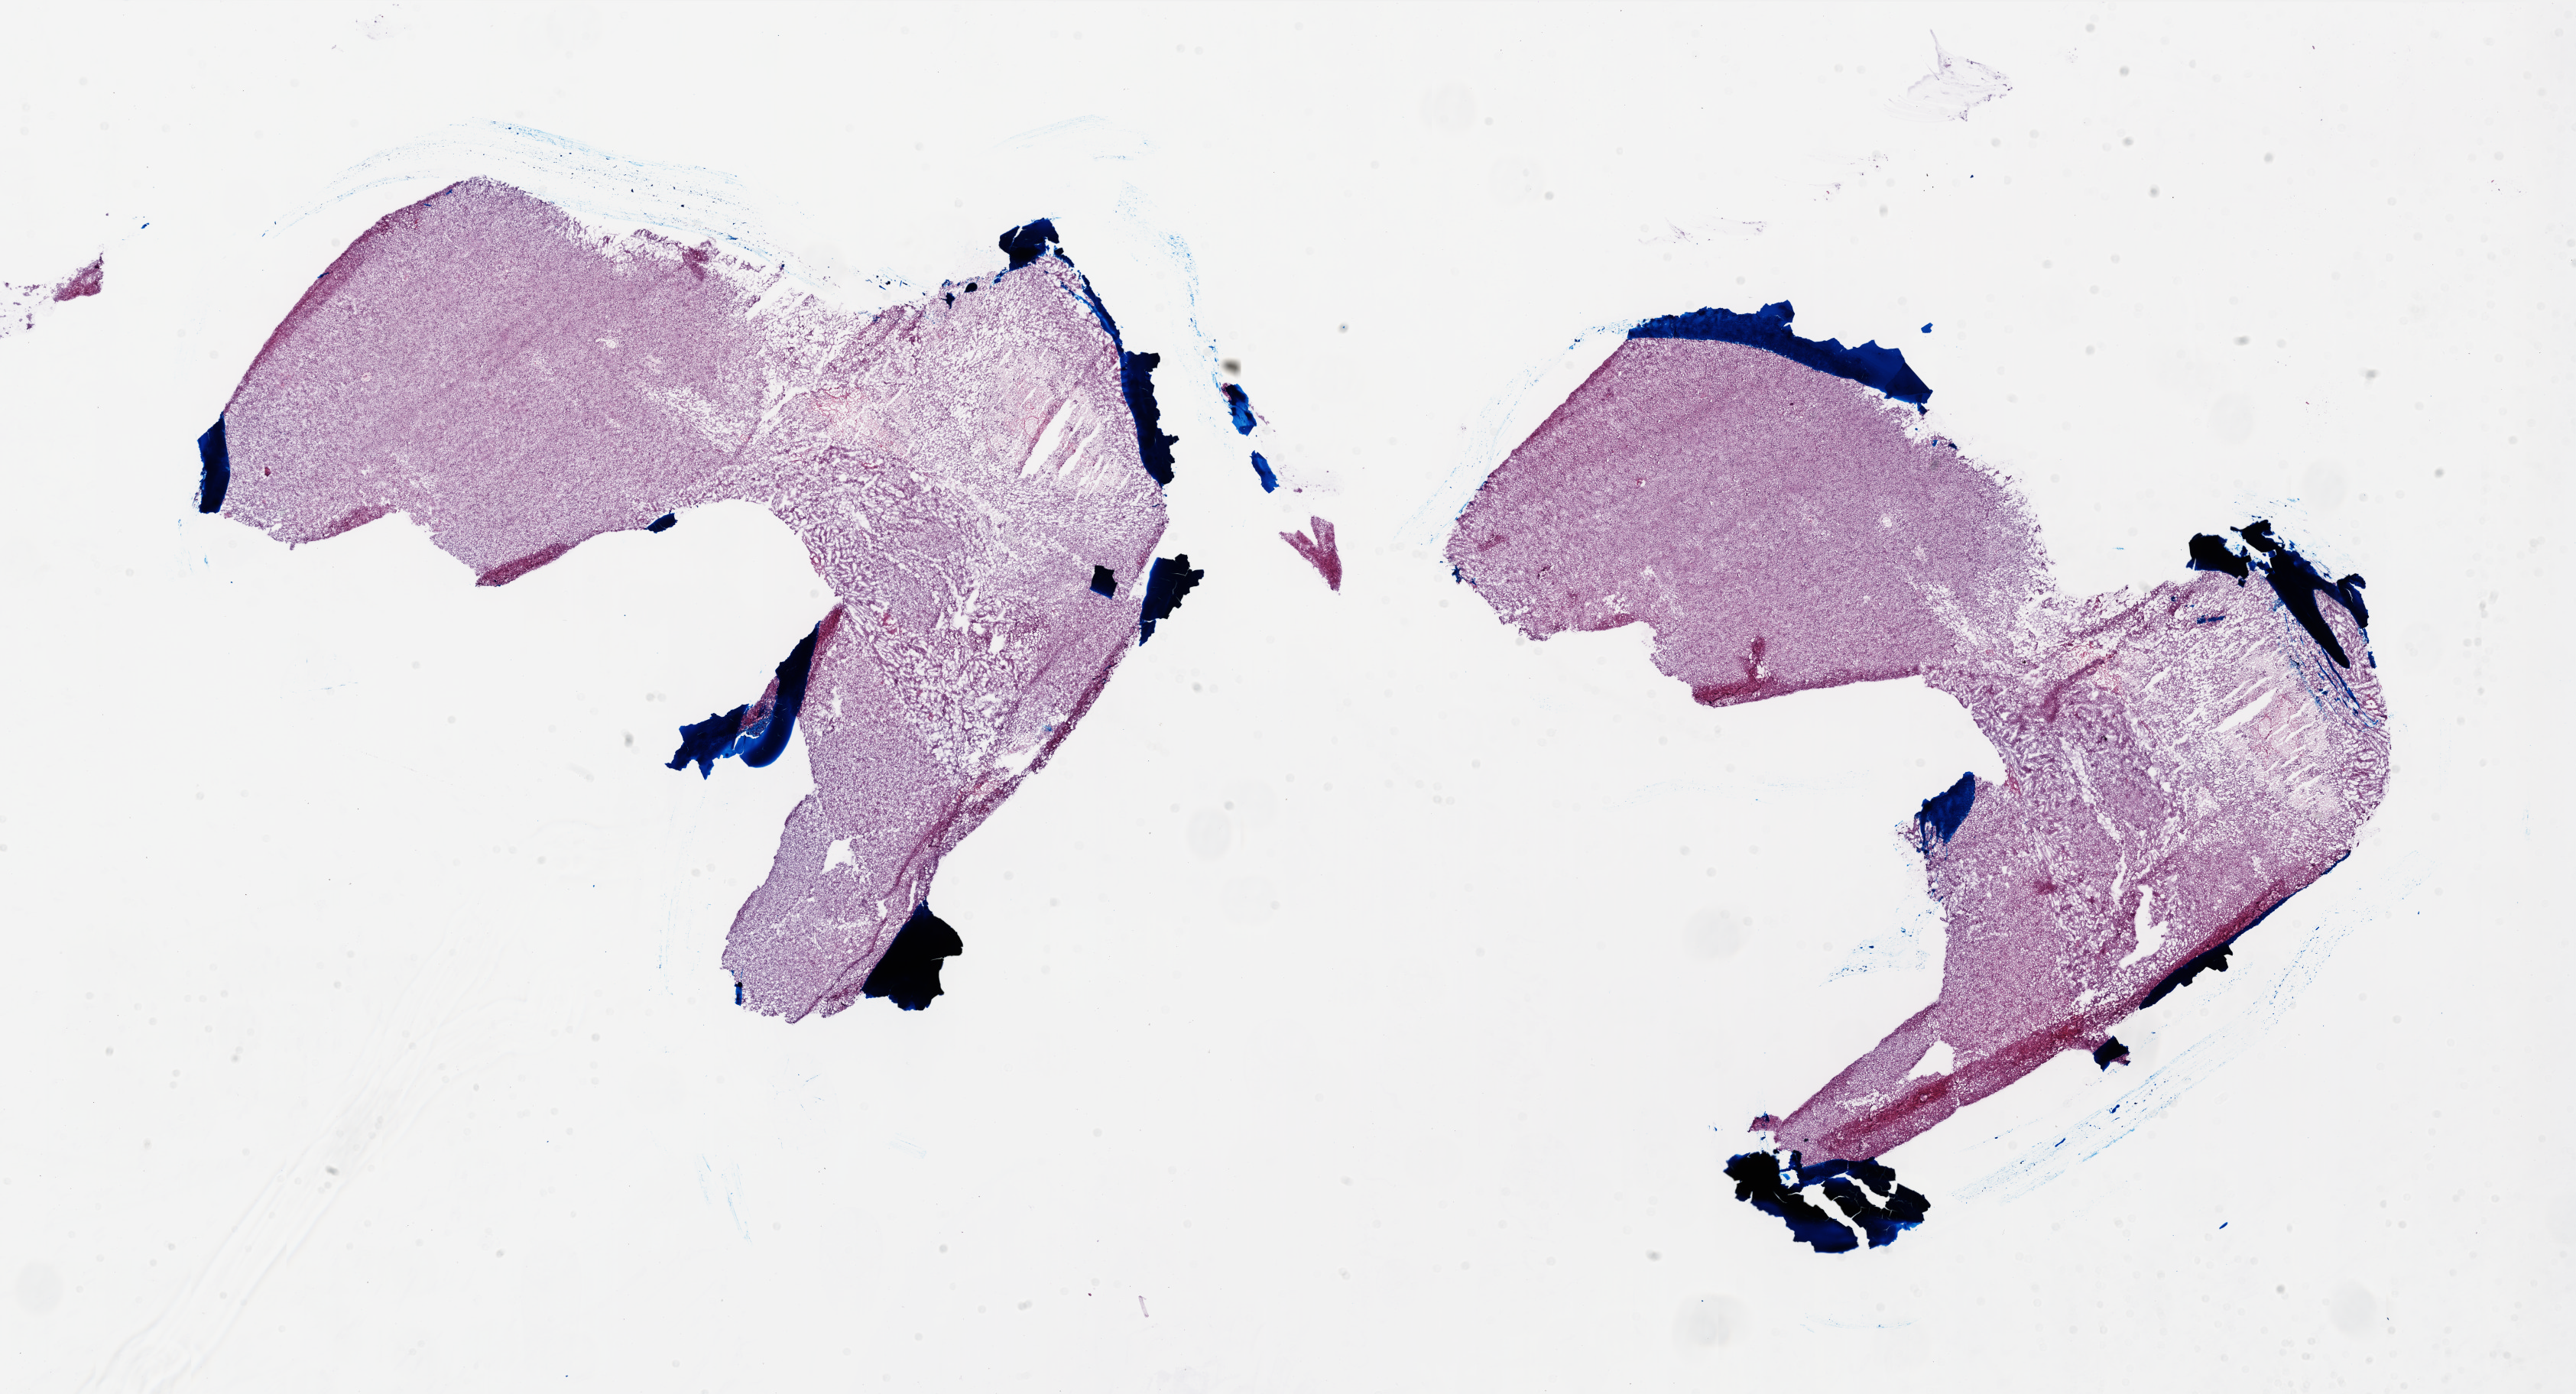
H&E whole-slide image, low-resolution overview of the scanned area, about 27.0 x 14.6 mm (from a 20x scan); frozen section from the top of the tissue portion; sample: primary tumour, brain. Female, age 52 years at initial diagnosis.
Pathologic diagnosis: Glioblastoma.